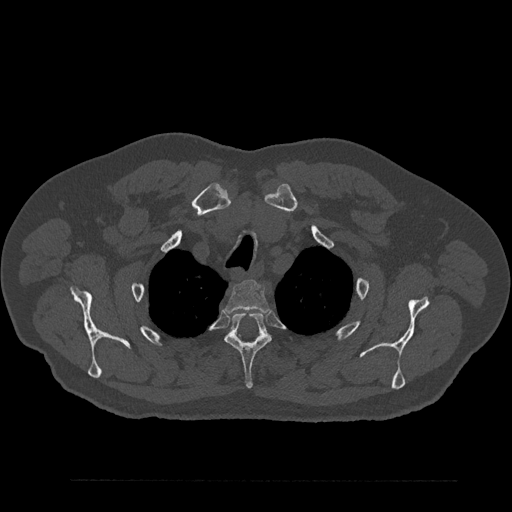
CT including the spine, one axial slice. Slice 687 of 797 in the series (ordered by position). Reconstruction kernel Br40s/3. 120 kVp. Bone window (W 1800 / L 400 HU). 512 × 512 image matrix, field of view 430 × 430 mm. Patient: male, 61 years. Case-level facts recorded for this patient, not image findings: primary cancer: prostate.
Annotated regions visible in this slice (semi-automatically segmented with operator editing):
- T2 vertebra: box from (x=225, y=280) to (x=269, y=312) px
- T3 vertebra: (x=224, y=312)–(x=272, y=389)